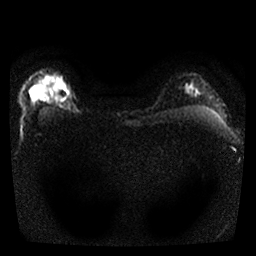
Breast MRI, one axial slice. Position 24 of 25 along the scan axis. Diffusion-weighted series; image 2 of 4 stored at this slice position (different b-values; order by instance number). 1.5 T. 4 mm slice thickness. 256 × 256 image matrix, field of view 300 × 300 mm. Female patient.
Outlined on this slice (manually delineated by an expert):
- tumour on diffusion-weighted imaging: box from (x=30, y=83) to (x=65, y=101) px